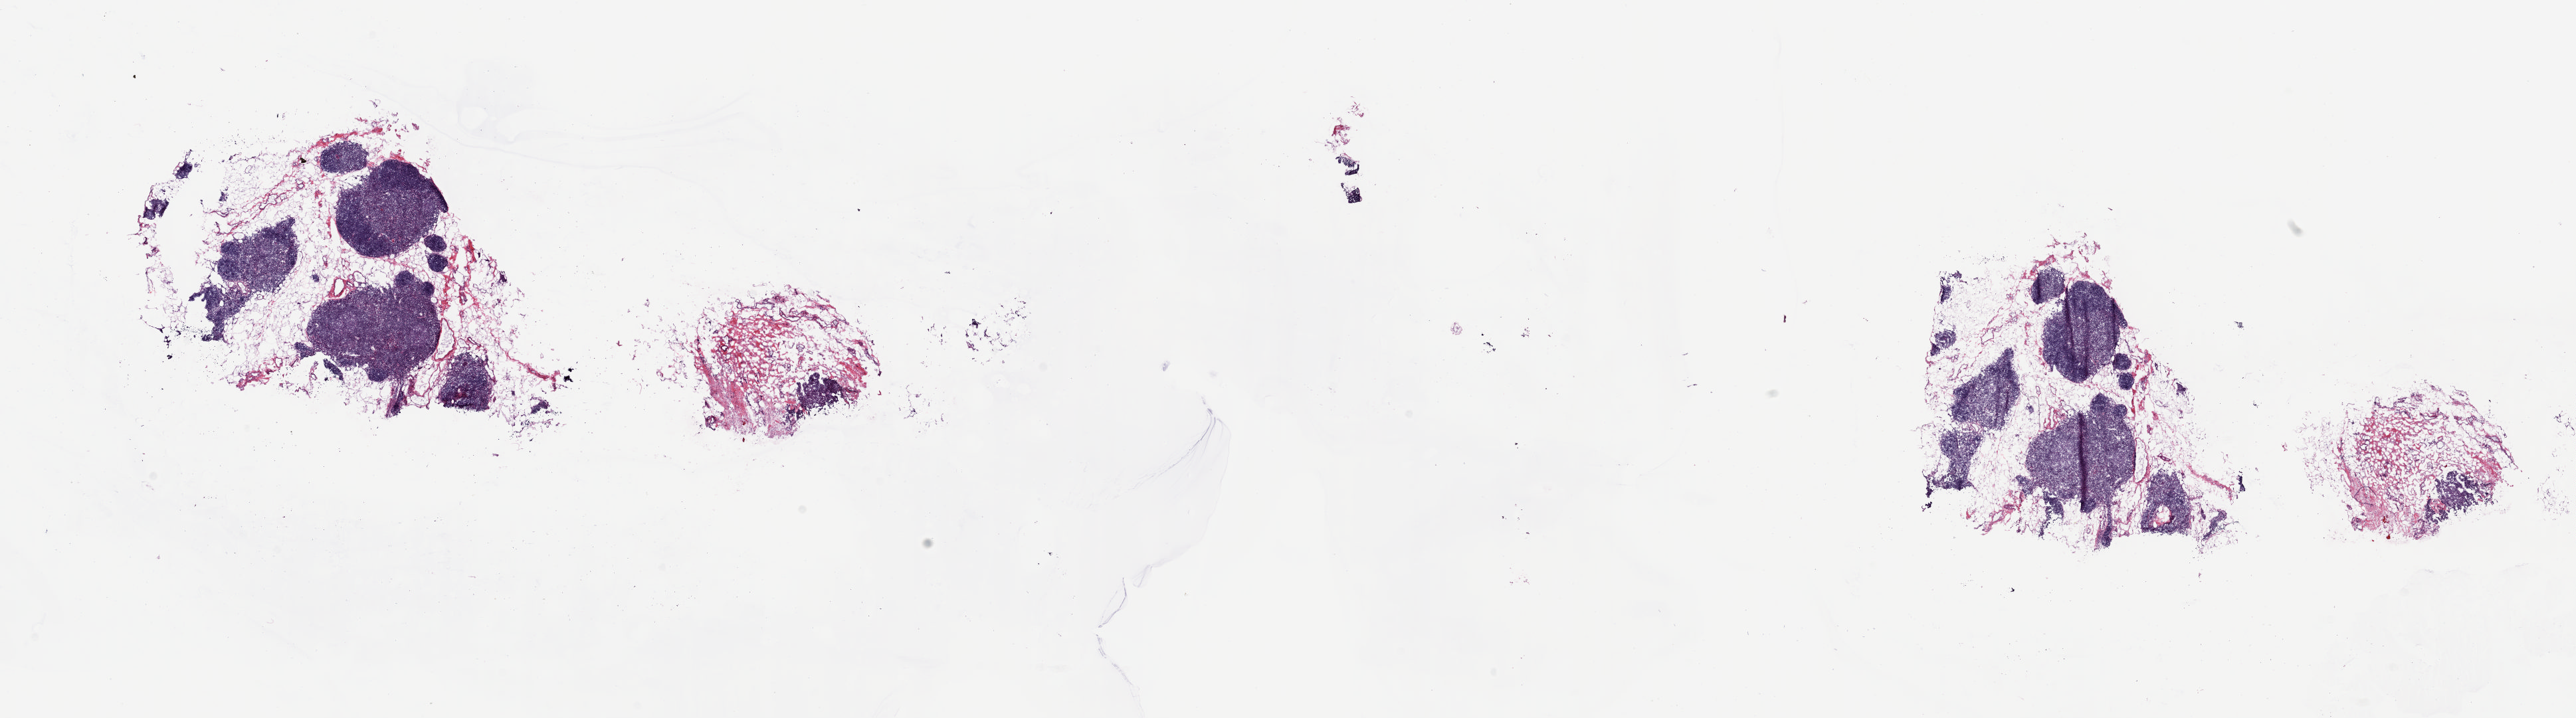
H&E whole-slide image — a low-resolution overview of the entire scanned area, about 30.7 x 8.6 mm, frozen section, sample: solid tissue normal (non-tumour tissue), thymus. Patient: female, age at initial diagnosis 58 years. Slide review estimates, as recorded: tumour cells 0%, tumour nuclei 0%, normal cells 0%, stromal cells 100%, necrosis 0%. Inflammatory infiltration, as recorded: lymphocyte infiltration 80%, monocyte infiltration 2%, neutrophil infiltration 2%.
This section: solid tissue normal sample (biorepository sample class). Patient diagnosis: Thymoma, type AB, malignant.